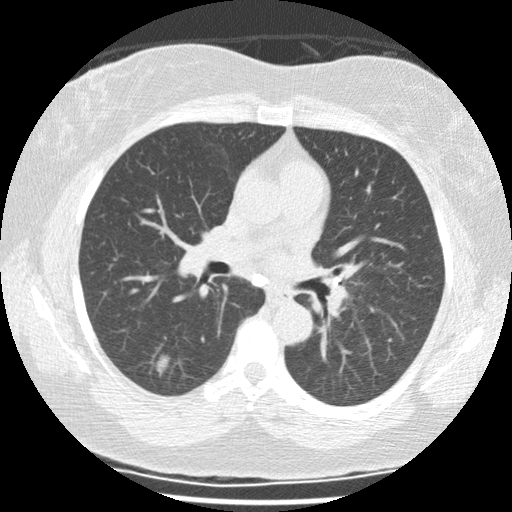
Axial slice from a low-dose chest CT screening exam, second screening round (one year after baseline), lung window (W 1500 / L -600 HU), 120 kVp. Female, age 65 years at enrolment.
• Expert-annotated lung lesion, bounding box [x1, y1, x2, y2] px = [138, 345, 182, 387].
• Reader record for this screening exam (exam-level; its link to the box is not recorded): non-calcified nodule or mass ≥4 mm, right lower lobe, 12 × 8 mm, spiculated (stellate) margins, mixed attenuation, pre-existing on the prior screen: yes; interval growth: yes.
• Official screen result: positive, other.